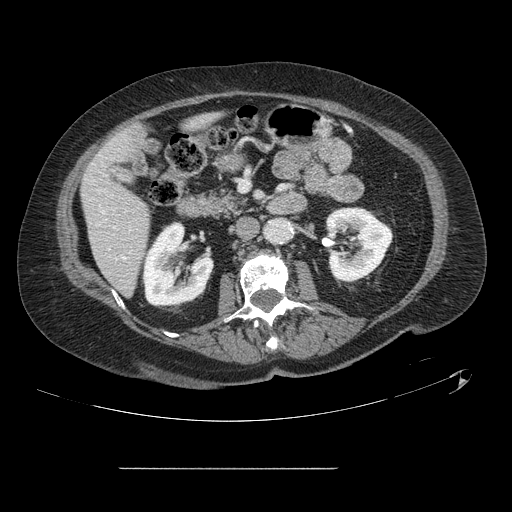
Contrast-enhanced abdominal CT, one axial slice; position 41 of 148 along the scan axis; 120 kVp; intravenous contrast given; soft-tissue window (W 400 / L 40 HU); 512 × 512 image matrix, field of view 439 × 439 mm. Female patient, age 75 years. From the clinical record (not read from this slice): diagnosis: colorectal cancer liver metastases, imaged before liver resection; multiple liver metastases: no; largest metastasis: 2.4 cm; disease in both lobes: no.
Structures marked on this image (outlined manually by an expert reader):
- hepatic veins: bounding box (x1, y1, x2, y2) in pixels: (103, 212, 125, 259)
- liver: (82, 116, 217, 295)
- planned liver remnant (the part of the liver to remain after resection): (82, 116, 217, 295)